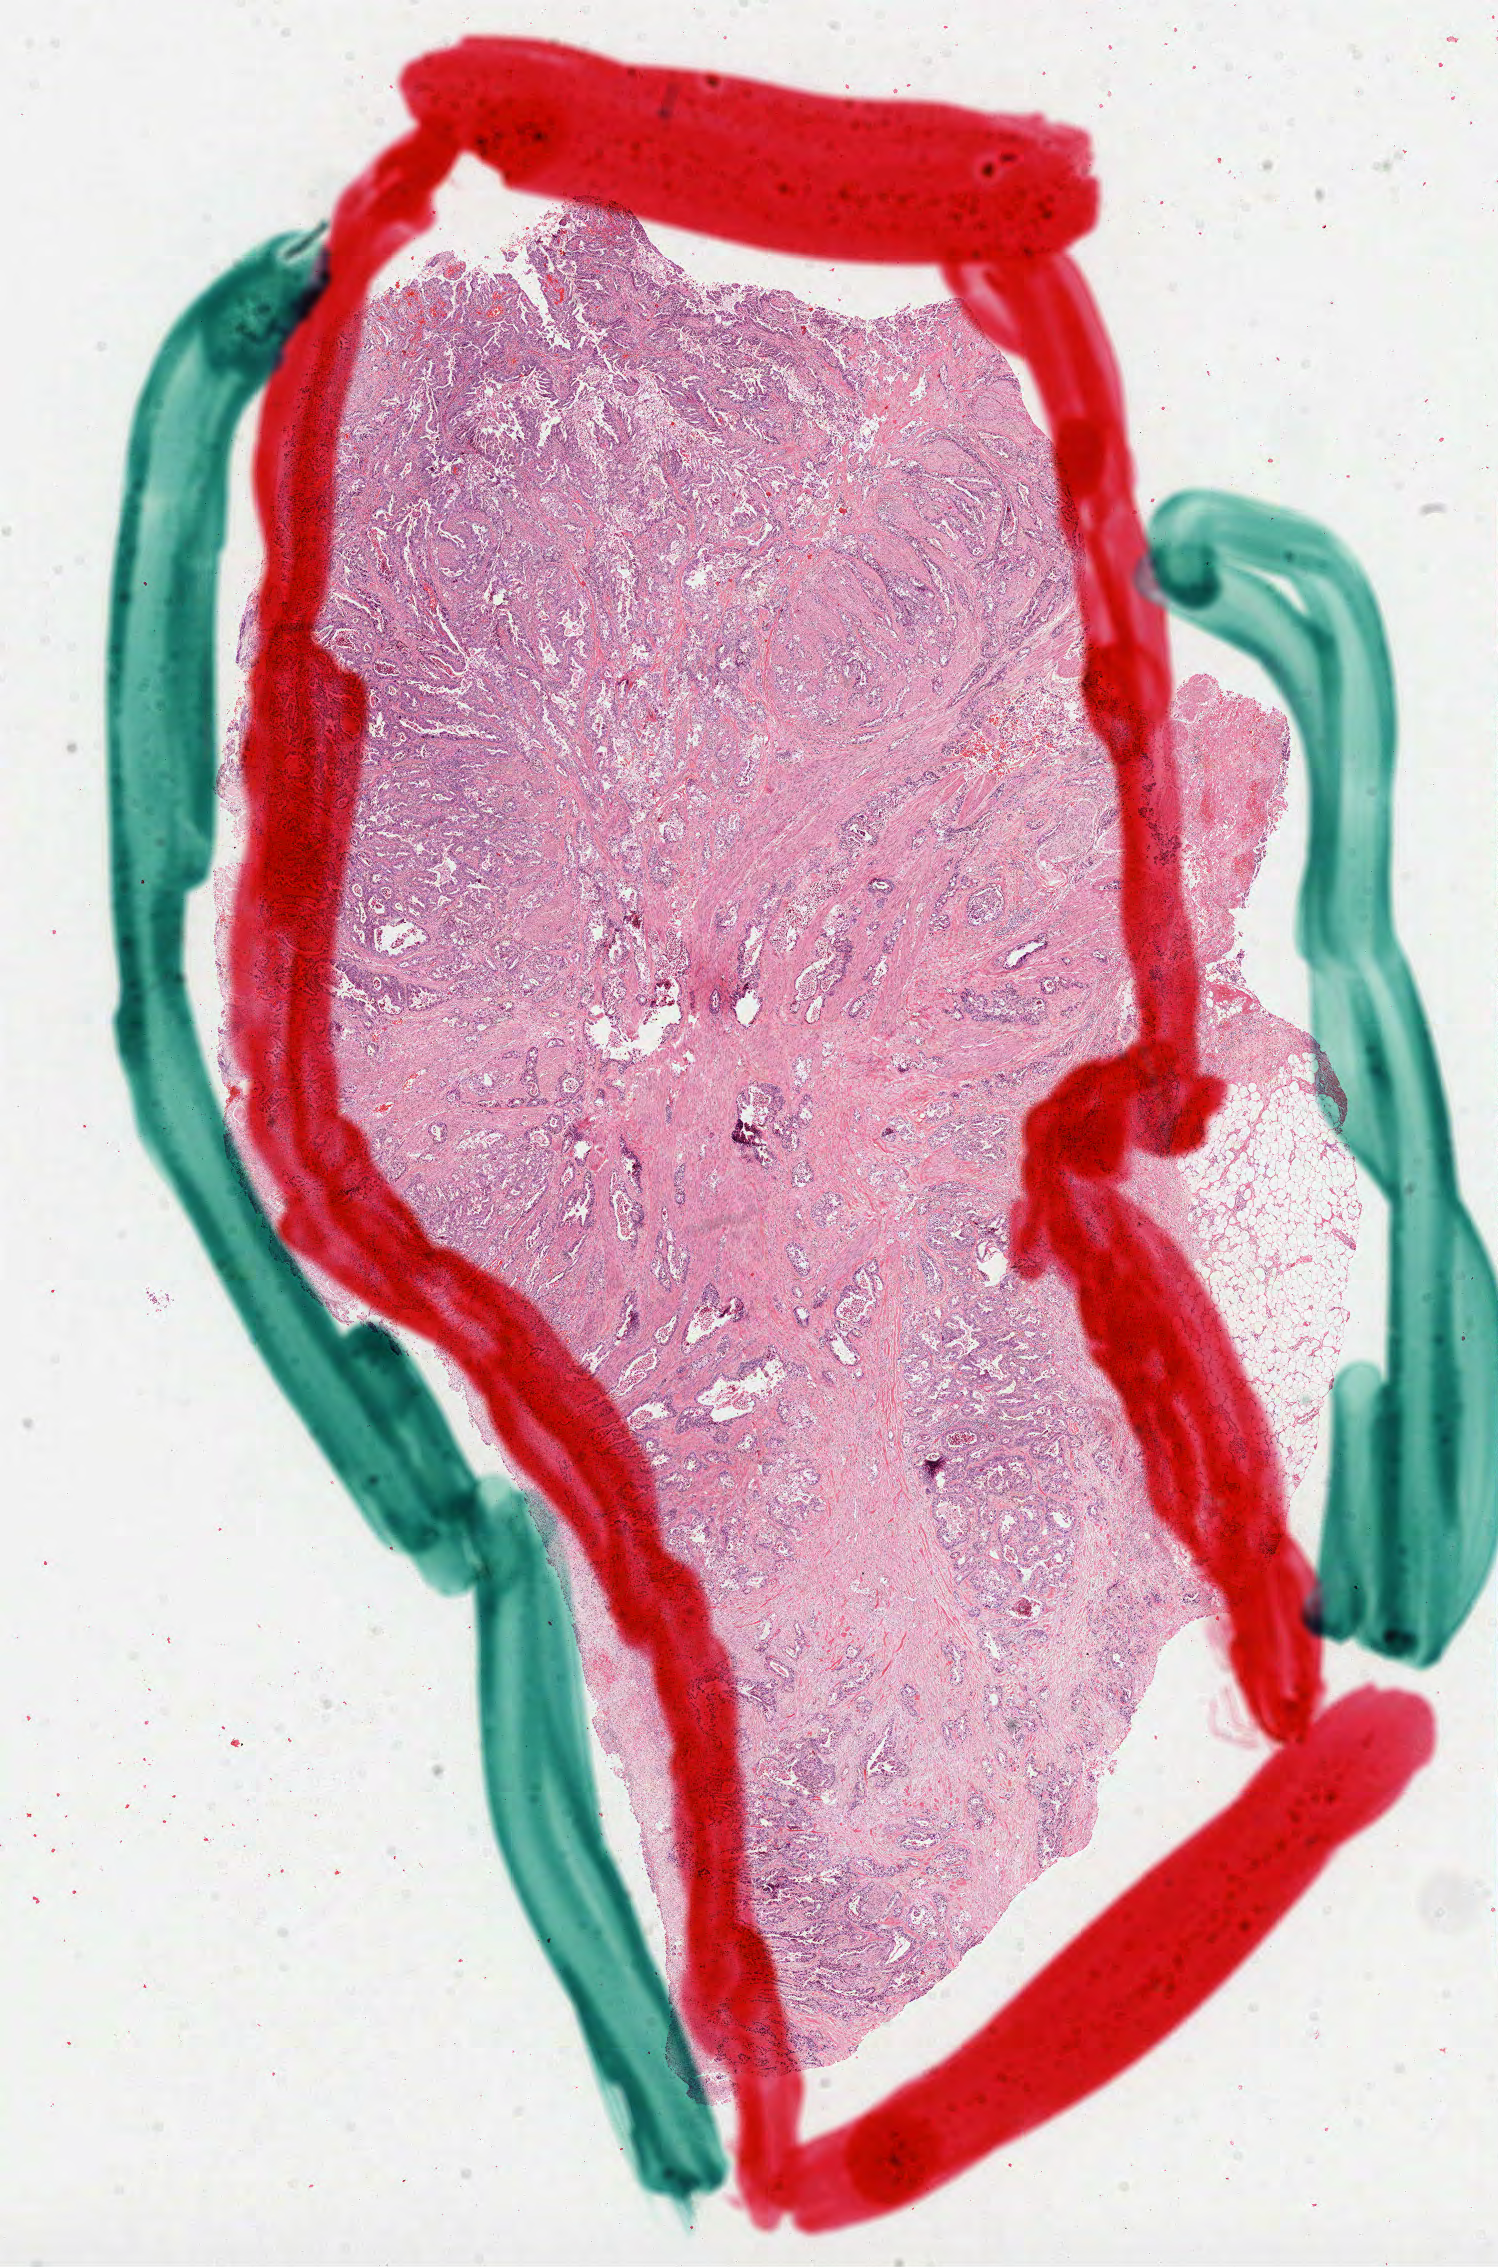
Whole-slide histology image, H&E — low-resolution overview of the scanned area, about 12.1 x 18.3 mm. Formalin-fixed paraffin-embedded (FFPE) diagnostic section. Primary tumour sample from the stomach. Patient: male, age at initial diagnosis 63 years. Histologic grade: G2 (moderately differentiated).
• histologic diagnosis: Adenocarcinoma, NOS (cardia, NOS)
• lymph nodes positive (case pathology): 2 of 6 examined
• AJCC pathologic stage: IV